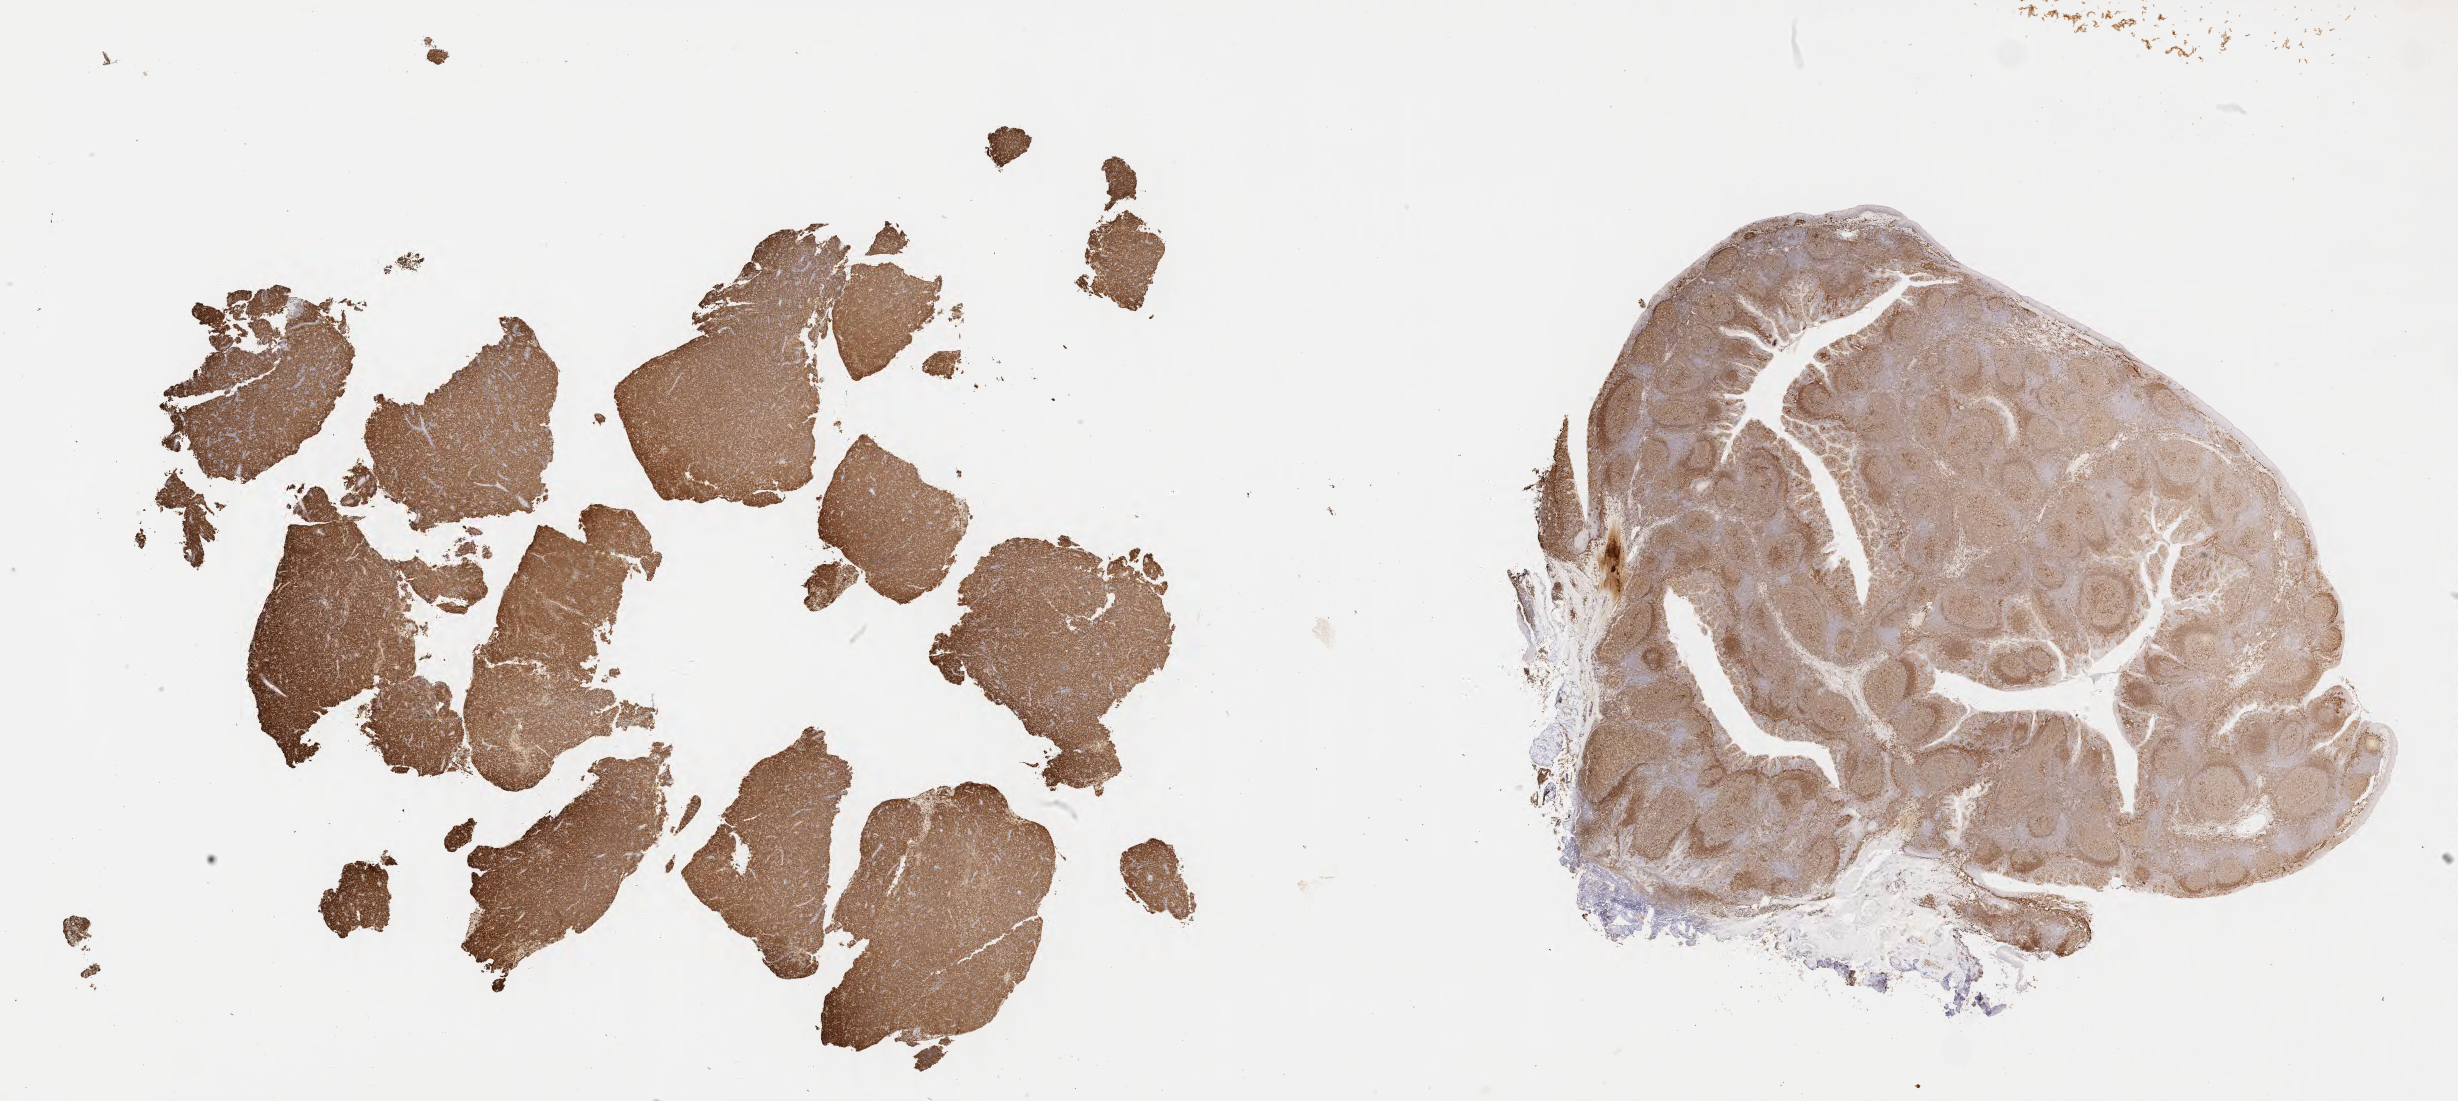
Whole-slide image, immunohistochemical stain for CD79a — whole scanned area (about 39.7 x 17.8 mm) shown as a low-resolution overview. Tumor tissue. Site: lymph node. Patient: female, aged 50.
Diagnosis: Diffuse large B-cell lymphoma, NOS.